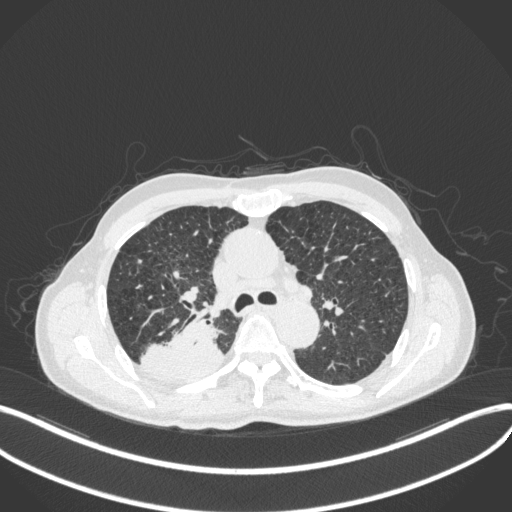
Chest CT, one axial slice; position 302 of 423 along the scan axis; 120 kVp; lung window (W 1500 / L -600 HU); 1 mm slice thickness; 512 × 512 image matrix, field of view 400 × 400 mm. Patient: male, 79 years. Case-level facts recorded for this patient, not image findings: clinical TNM (as recorded): T3 N0 M0.
Structures marked on this image (bounding box drawn by a radiologist):
- lung tumour (recorded histology: adenocarcinoma): bounding box <142,314,226,386> (left, top, right, bottom; pixels)